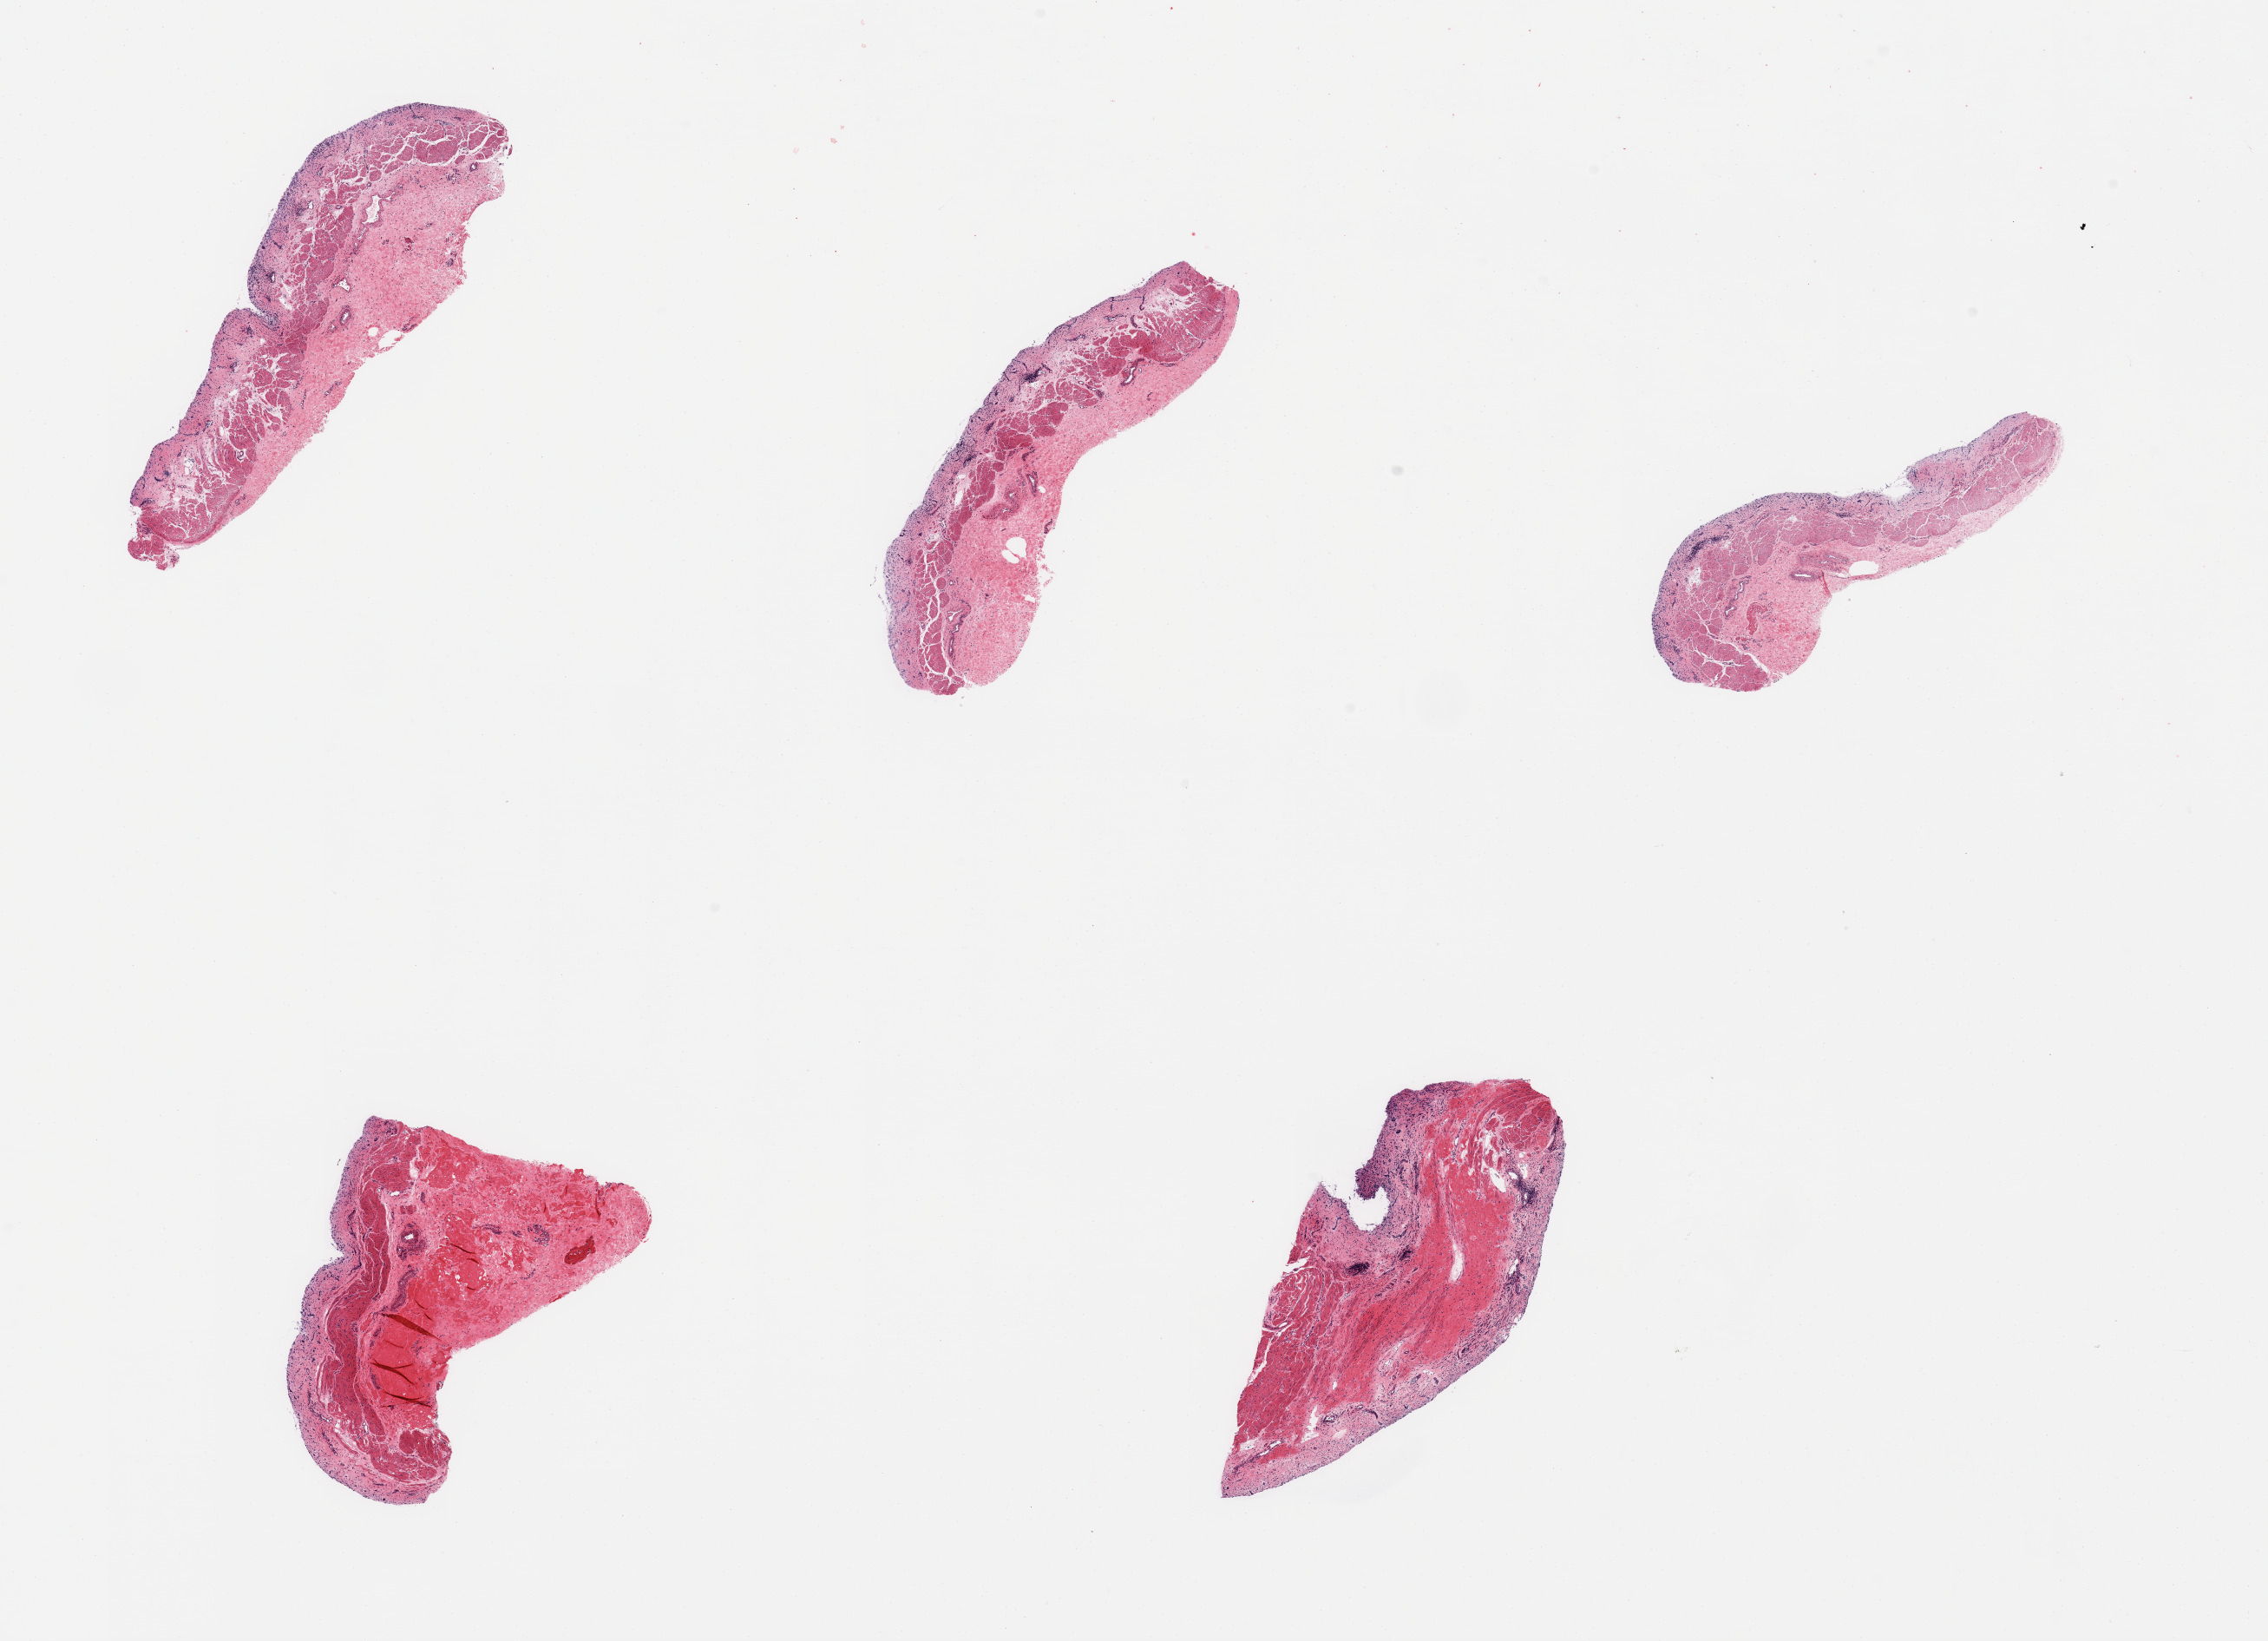
H&E whole-slide image, brightfield — low-resolution overview of the scanned area, about 20.7 x 15.0 mm; PAXgene-fixed paraffin-embedded (PFPE) section; section of esophageal mucous membrane (target tissue); tissue donor sample. Male donor.
Reviewer comment on this tissue sample: 5 pieces, no target squamous mucosa.